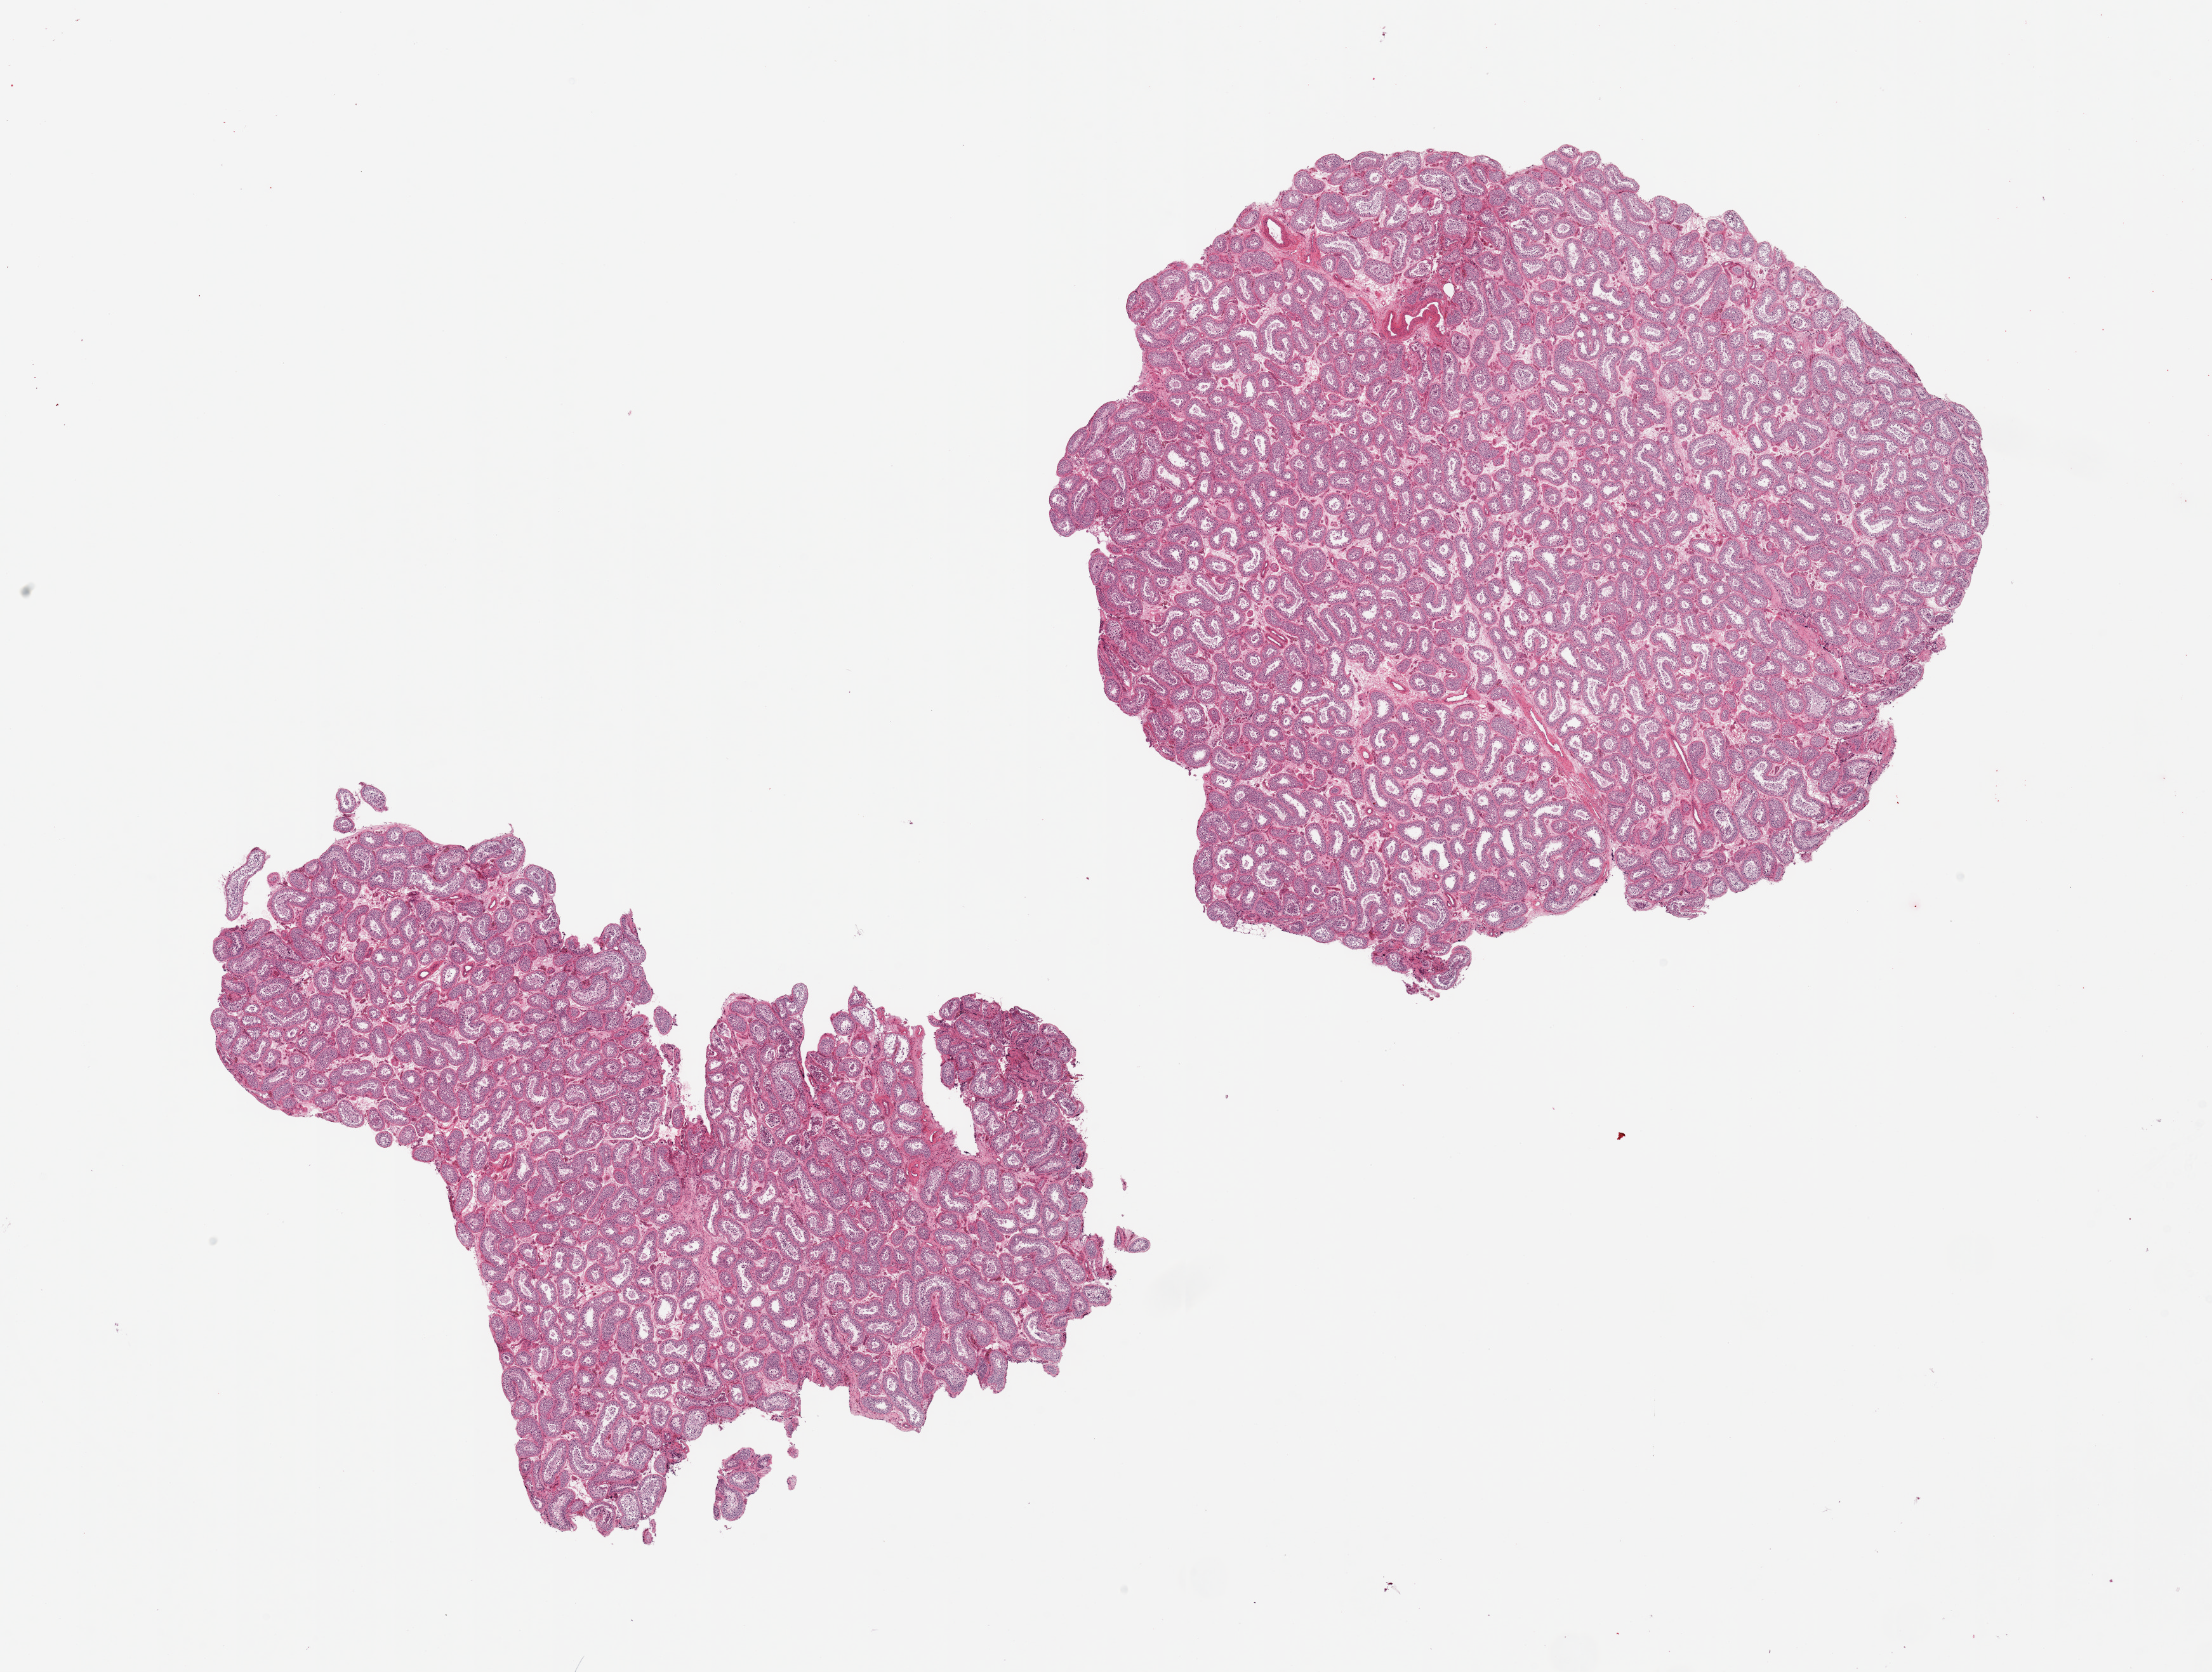
Whole-slide image, haematoxylin and eosin stain — low-resolution overview of the scanned area, about 27.6 x 20.8 mm (slide scanned at 20x). PAXgene-fixed paraffin-embedded (PFPE) section. Sampled site (target tissue): testis. Donor tissue sample. Donor sex: male.
Pathologist's review note for this sample: 2 pieces. Spermatogenesis.